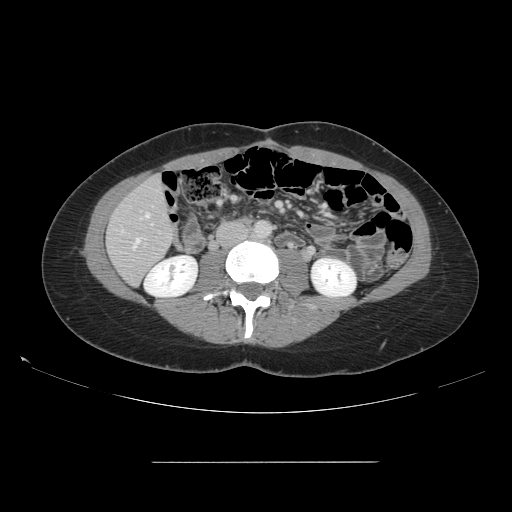
Contrast-enhanced abdominal CT, one axial slice. Position 42 of 151 along the scan axis. Intravenous contrast given. Soft-tissue window (W 400 / L 40 HU). 2.5 mm slice thickness. 512 × 512 image matrix. Female patient, age 46 years. Case-level facts recorded for this patient, not image findings: diagnosis: colorectal cancer liver metastases, imaged before liver resection; multiple liver metastases: yes; largest metastasis: 3 cm; disease in both lobes: yes.
Structures marked on this image (manually delineated by an expert):
- hepatic veins: bounding box [x1, y1, x2, y2] px = [134, 213, 149, 248]
- liver: [108, 177, 175, 285]
- planned liver remnant (the part of the liver to remain after resection): [108, 177, 175, 285]